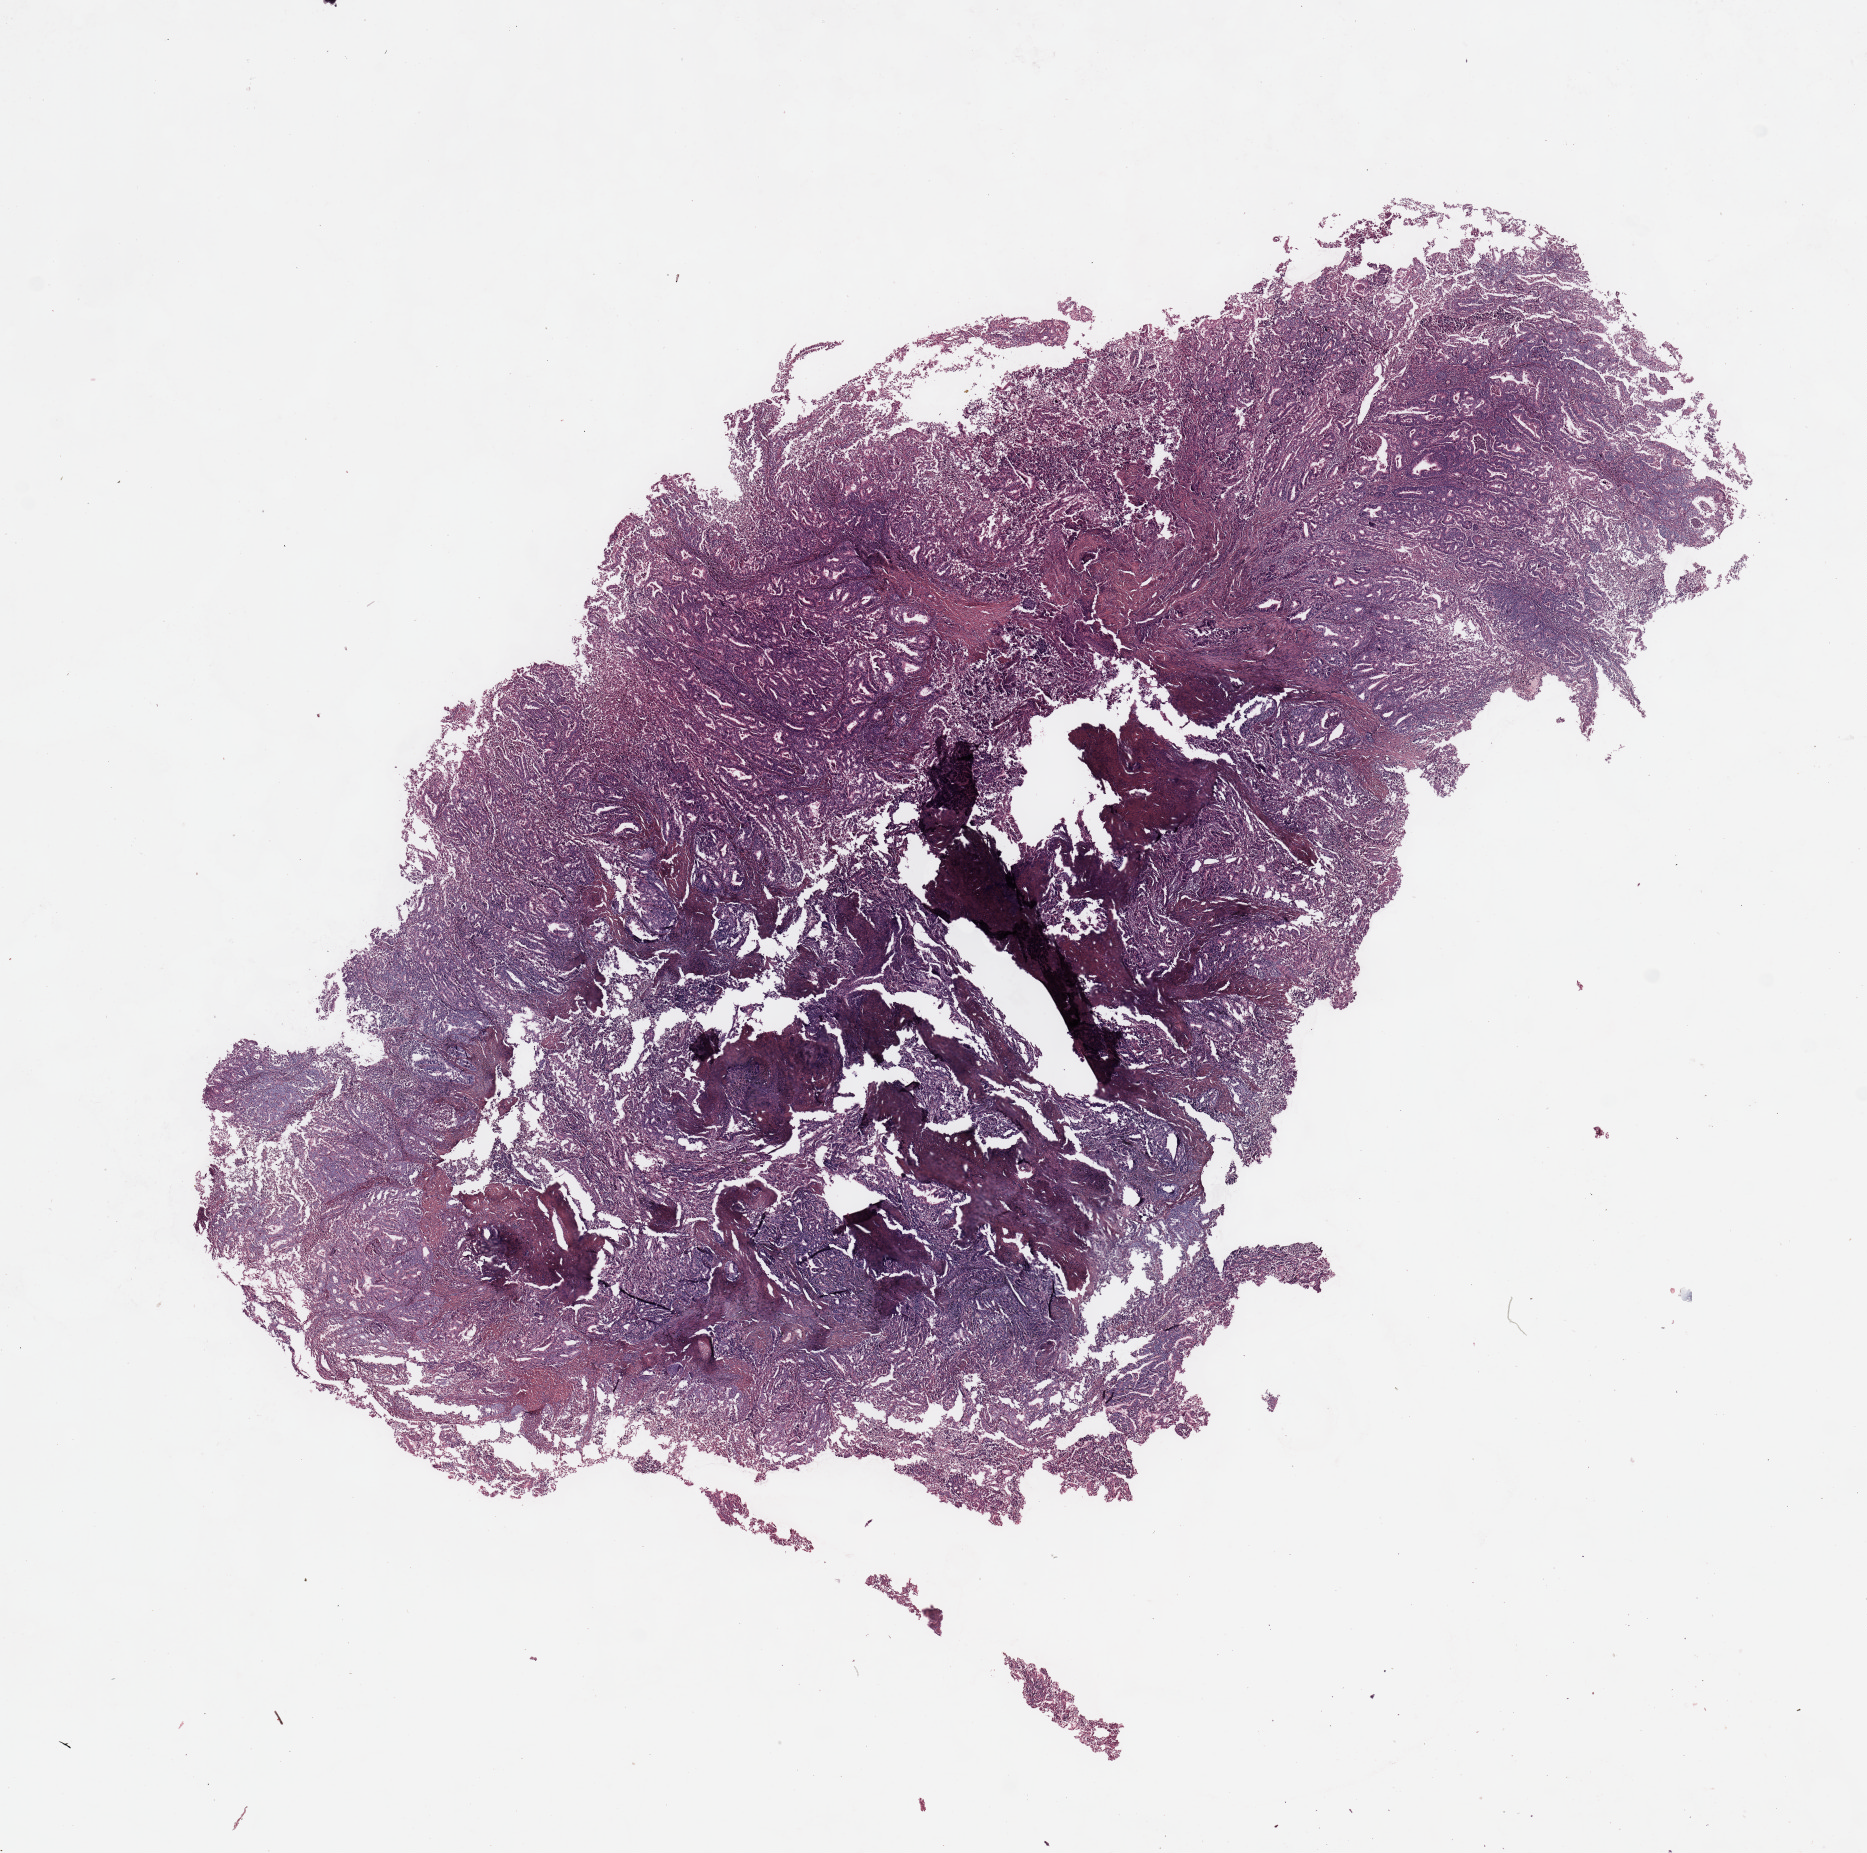
Digitized H&E-stained tissue section (whole slide), a low-resolution overview of the entire scanned area, about 14.8 x 14.7 mm; uterus, tumour tissue. Patient: female, age 70 years. Histologic grade: G2 (moderately differentiated).
AJCC pathologic stage: I. Histologic diagnosis: Endometrioid adenocarcinoma, NOS.